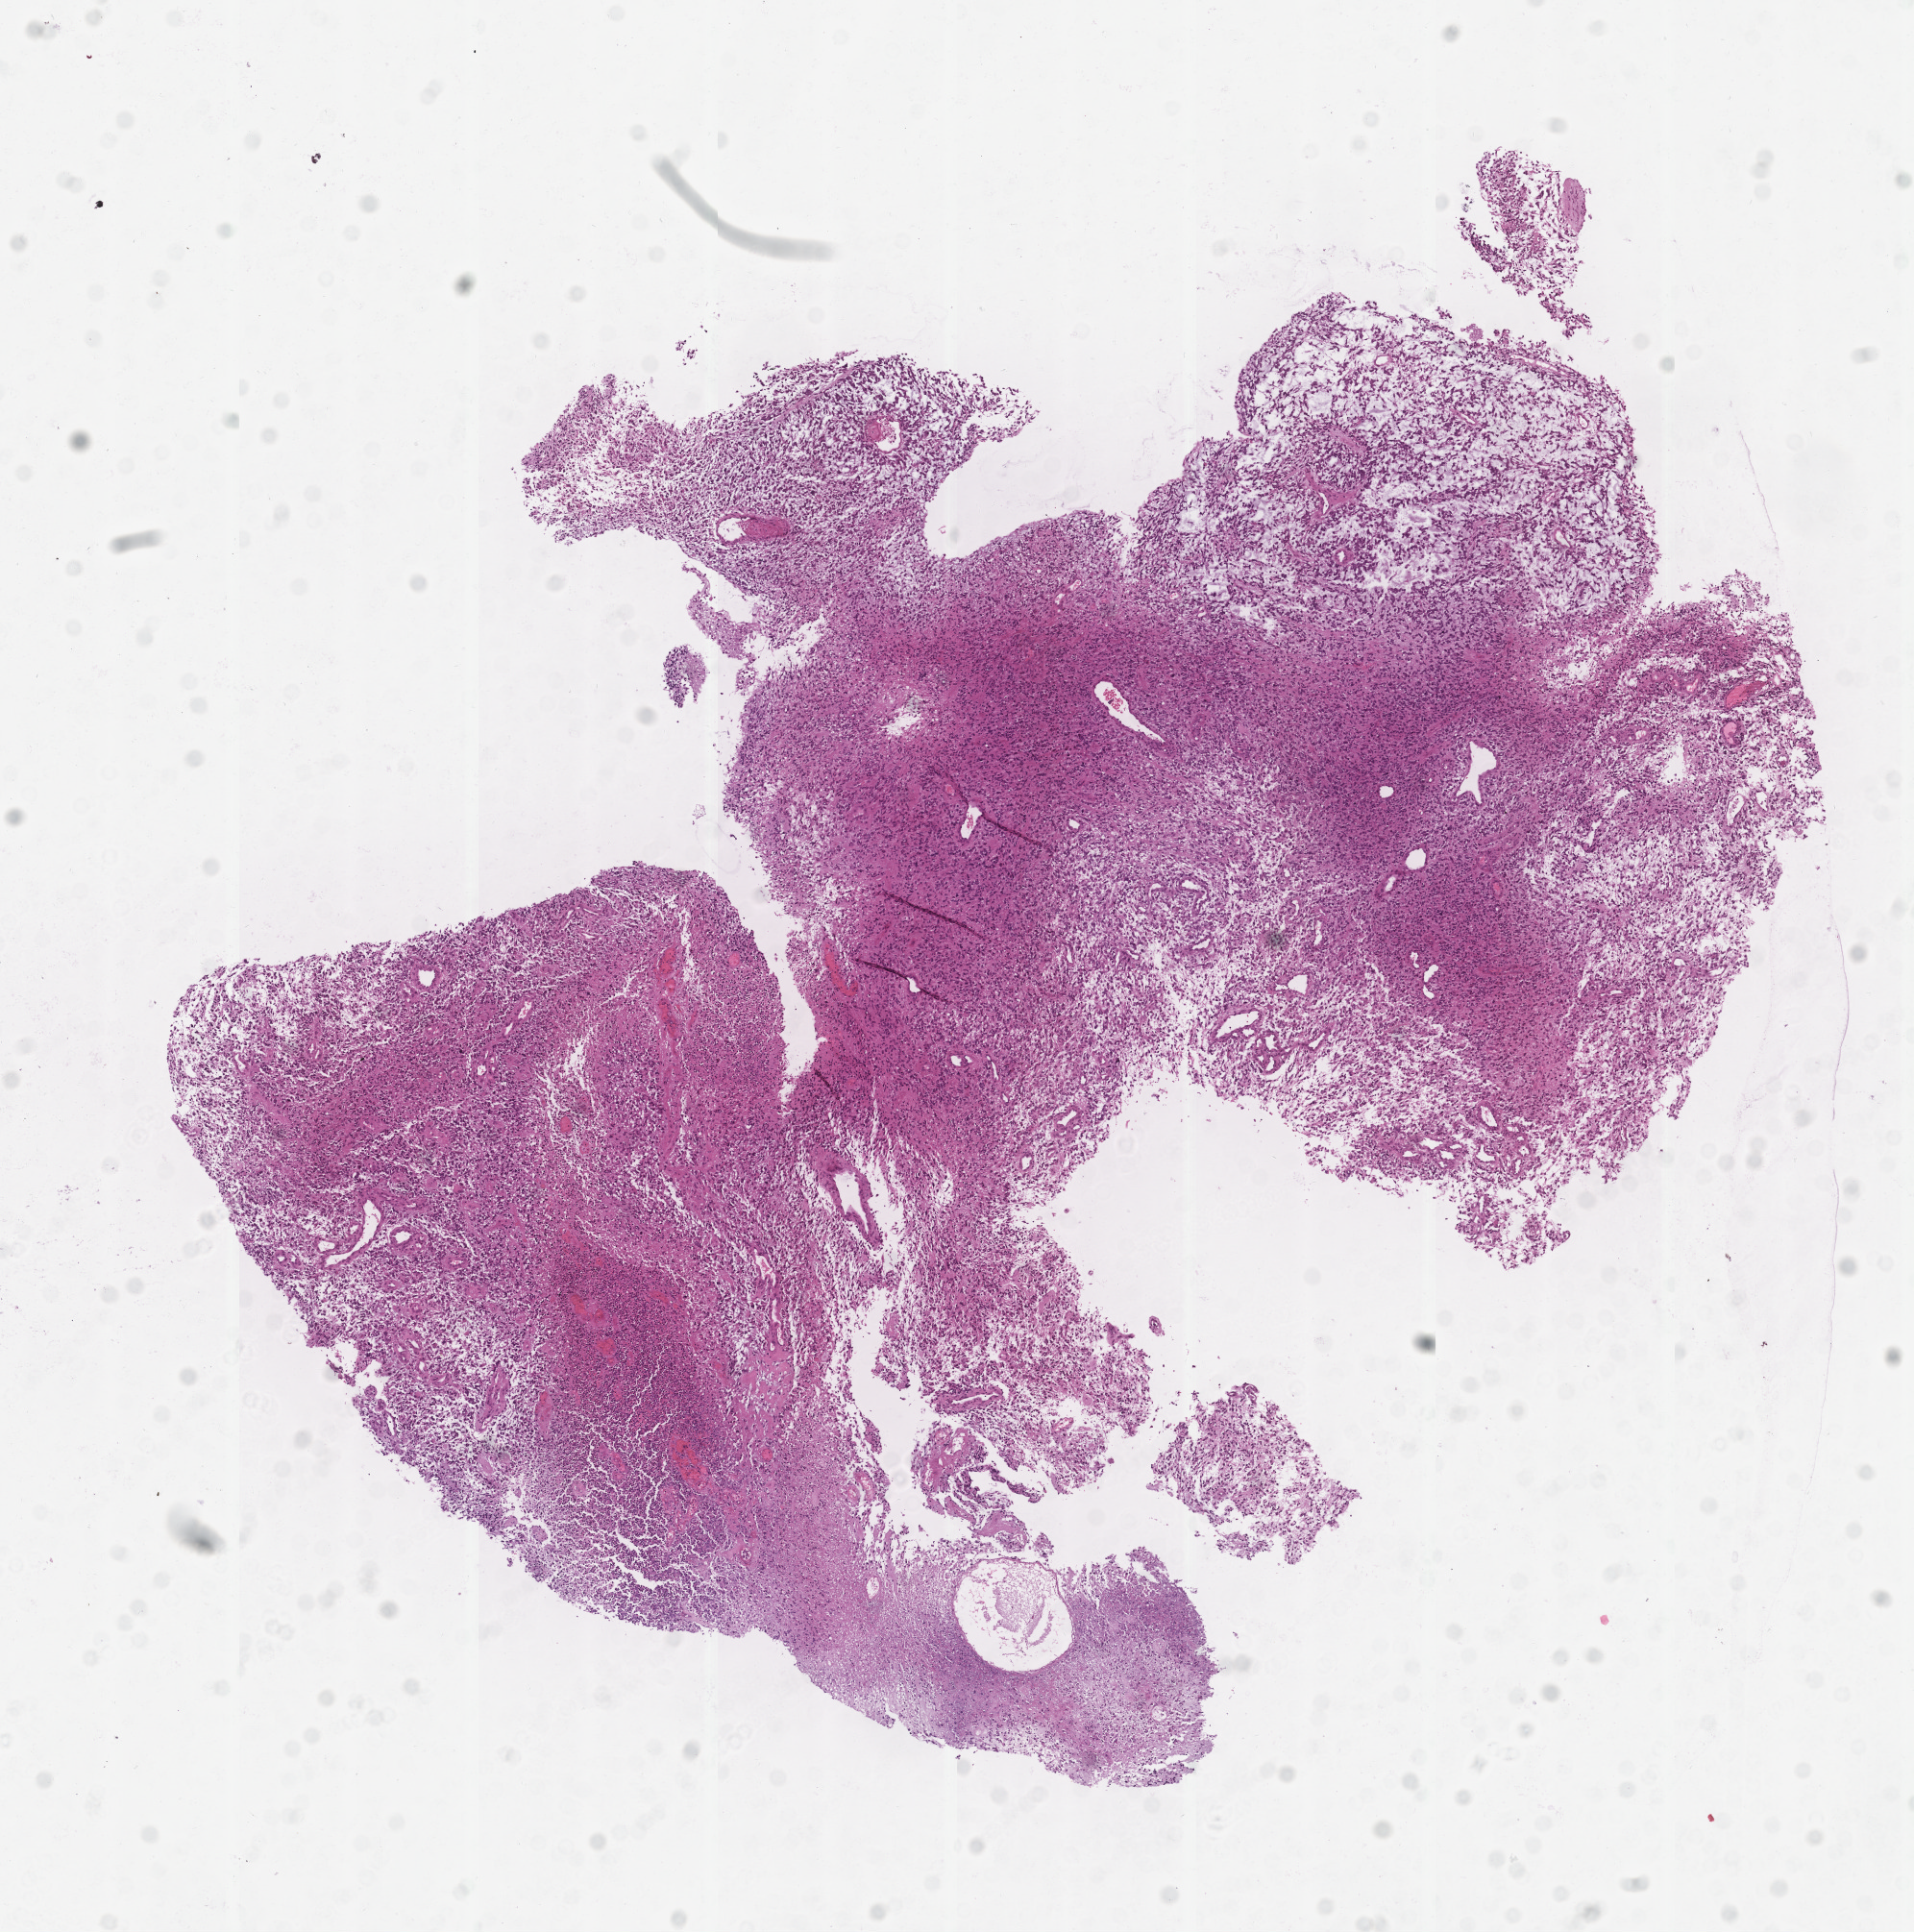
Digitized H&E-stained tissue section (whole slide), low-resolution overview of the scanned area, about 8.0 x 8.1 mm (slide scanned at 20x); tumour tissue sample, brain. 62-year-old male patient.
Histologic diagnosis: Glioblastoma.